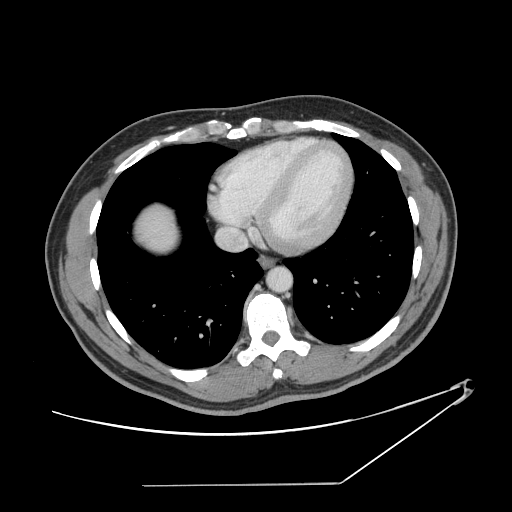
Contrast-enhanced abdominal CT, one axial slice; position 141 of 152 along the scan axis; intravenous contrast given; soft-tissue window (W 400 / L 40 HU); 512 × 512 image matrix, field of view 432 × 432 mm. Male patient, age 45 years. From the clinical record (not read from this slice): diagnosis: colorectal cancer liver metastases, imaged before liver resection; multiple liver metastases: no; largest metastasis: 1 cm; disease in both lobes: no.
Structures marked on this image (outlined manually by an expert reader):
- hepatic veins: bounding box [x1, y1, x2, y2] px = [233, 231, 247, 246]
- liver: [142, 207, 177, 250]
- planned liver remnant (the part of the liver to remain after resection): [141, 208, 178, 250]